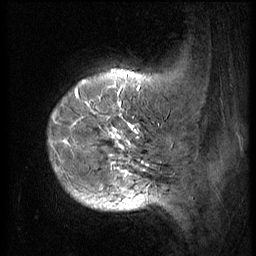
Breast MRI (dynamic contrast-enhanced), one sagittal slice. Position 11 of 56 along the scan axis. 3 images stored at this slice position (order not interpretable as contrast timing). 1.5 T. TE 4.2 ms, TR 9 ms. 2.5 mm slice thickness. 256 × 256 image matrix, field of view 180 × 180 mm. Female patient, age 49 years. From the clinical record (not read from this slice): setting: breast cancer imaged before/during neoadjuvant chemotherapy; receptor status: HER2-positive.
Structures marked on this image (semi-automatically segmented with operator editing):
- analysis volume of interest (the breast-tissue region the enhancement analysis was run in; not a lesion): bounding box (x1, y1, x2, y2) in pixels: (47, 79, 152, 203)
- tumour enhancement mask (voxels above the 140 % enhancement threshold inside the analysis volume of interest): (49, 79, 151, 203)